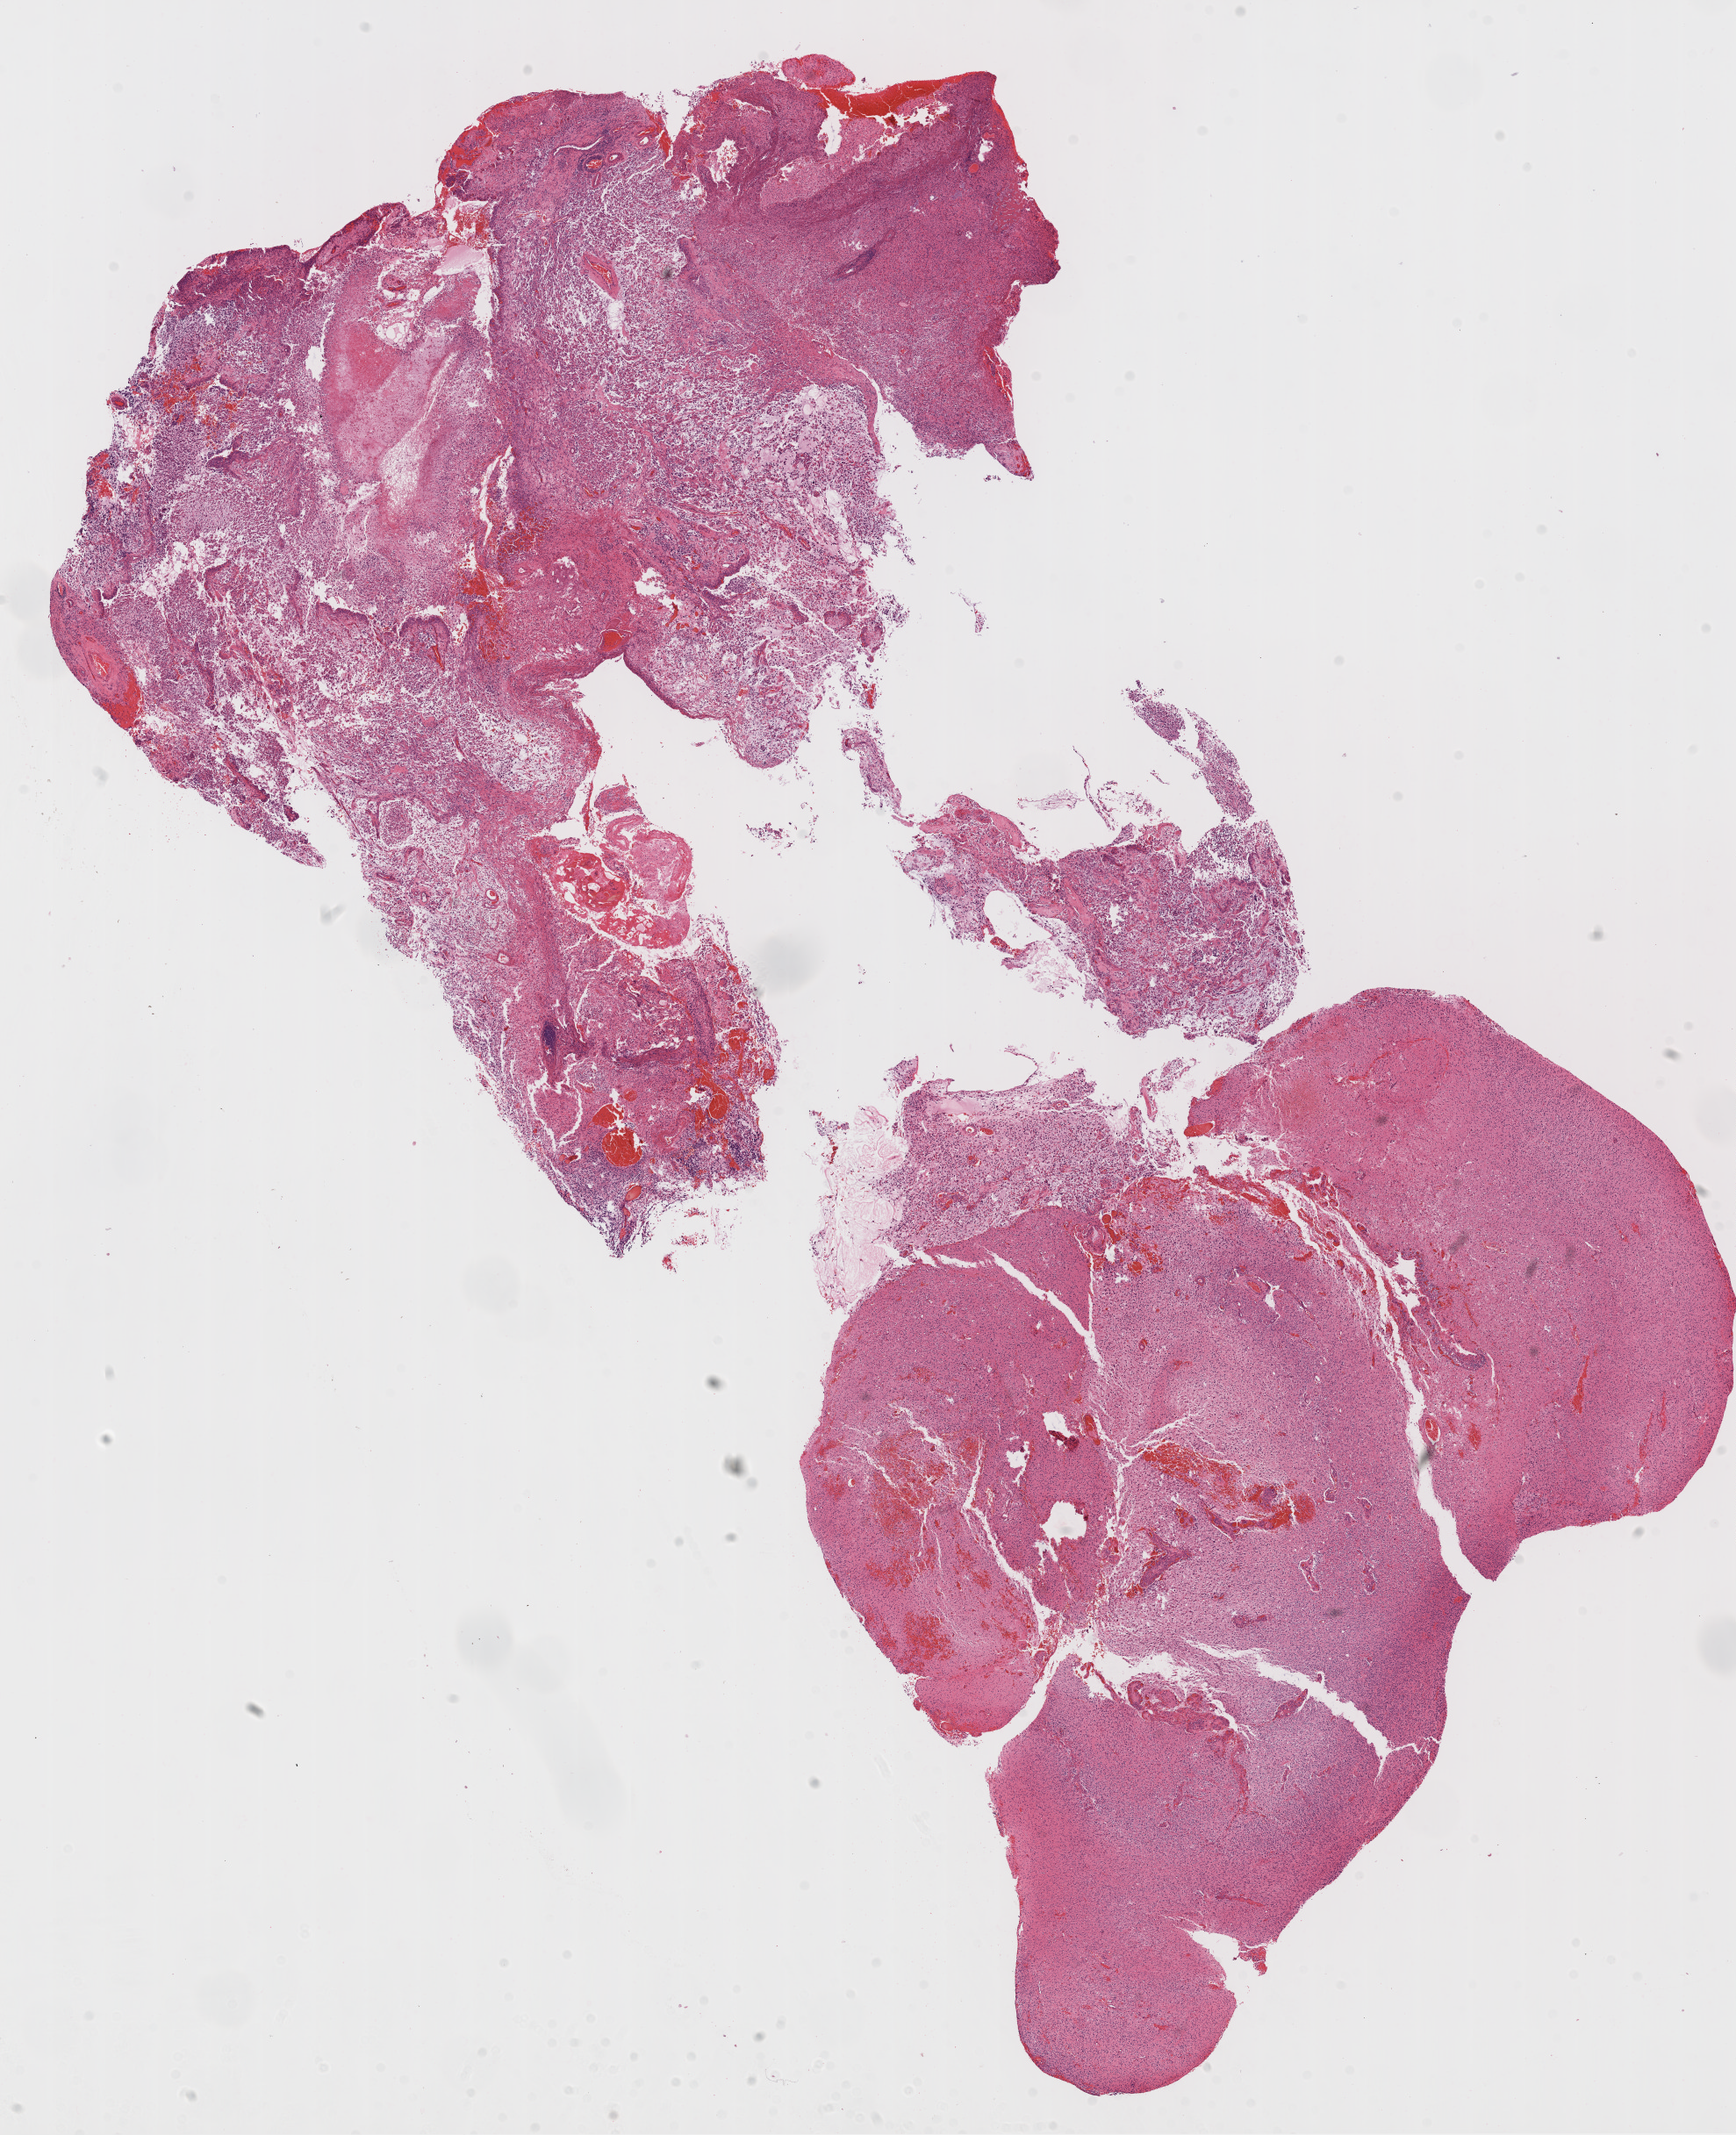
H&E-stained whole-slide image — shown as a low-resolution overview of the whole scanned area (about 16.0 x 19.6 mm, acquisition: 20x scan). Formalin-fixed paraffin-embedded (FFPE) diagnostic section. Sample: primary tumour, brain. Patient: male, age at initial diagnosis 66 years.
Pathologic diagnosis: Glioblastoma.